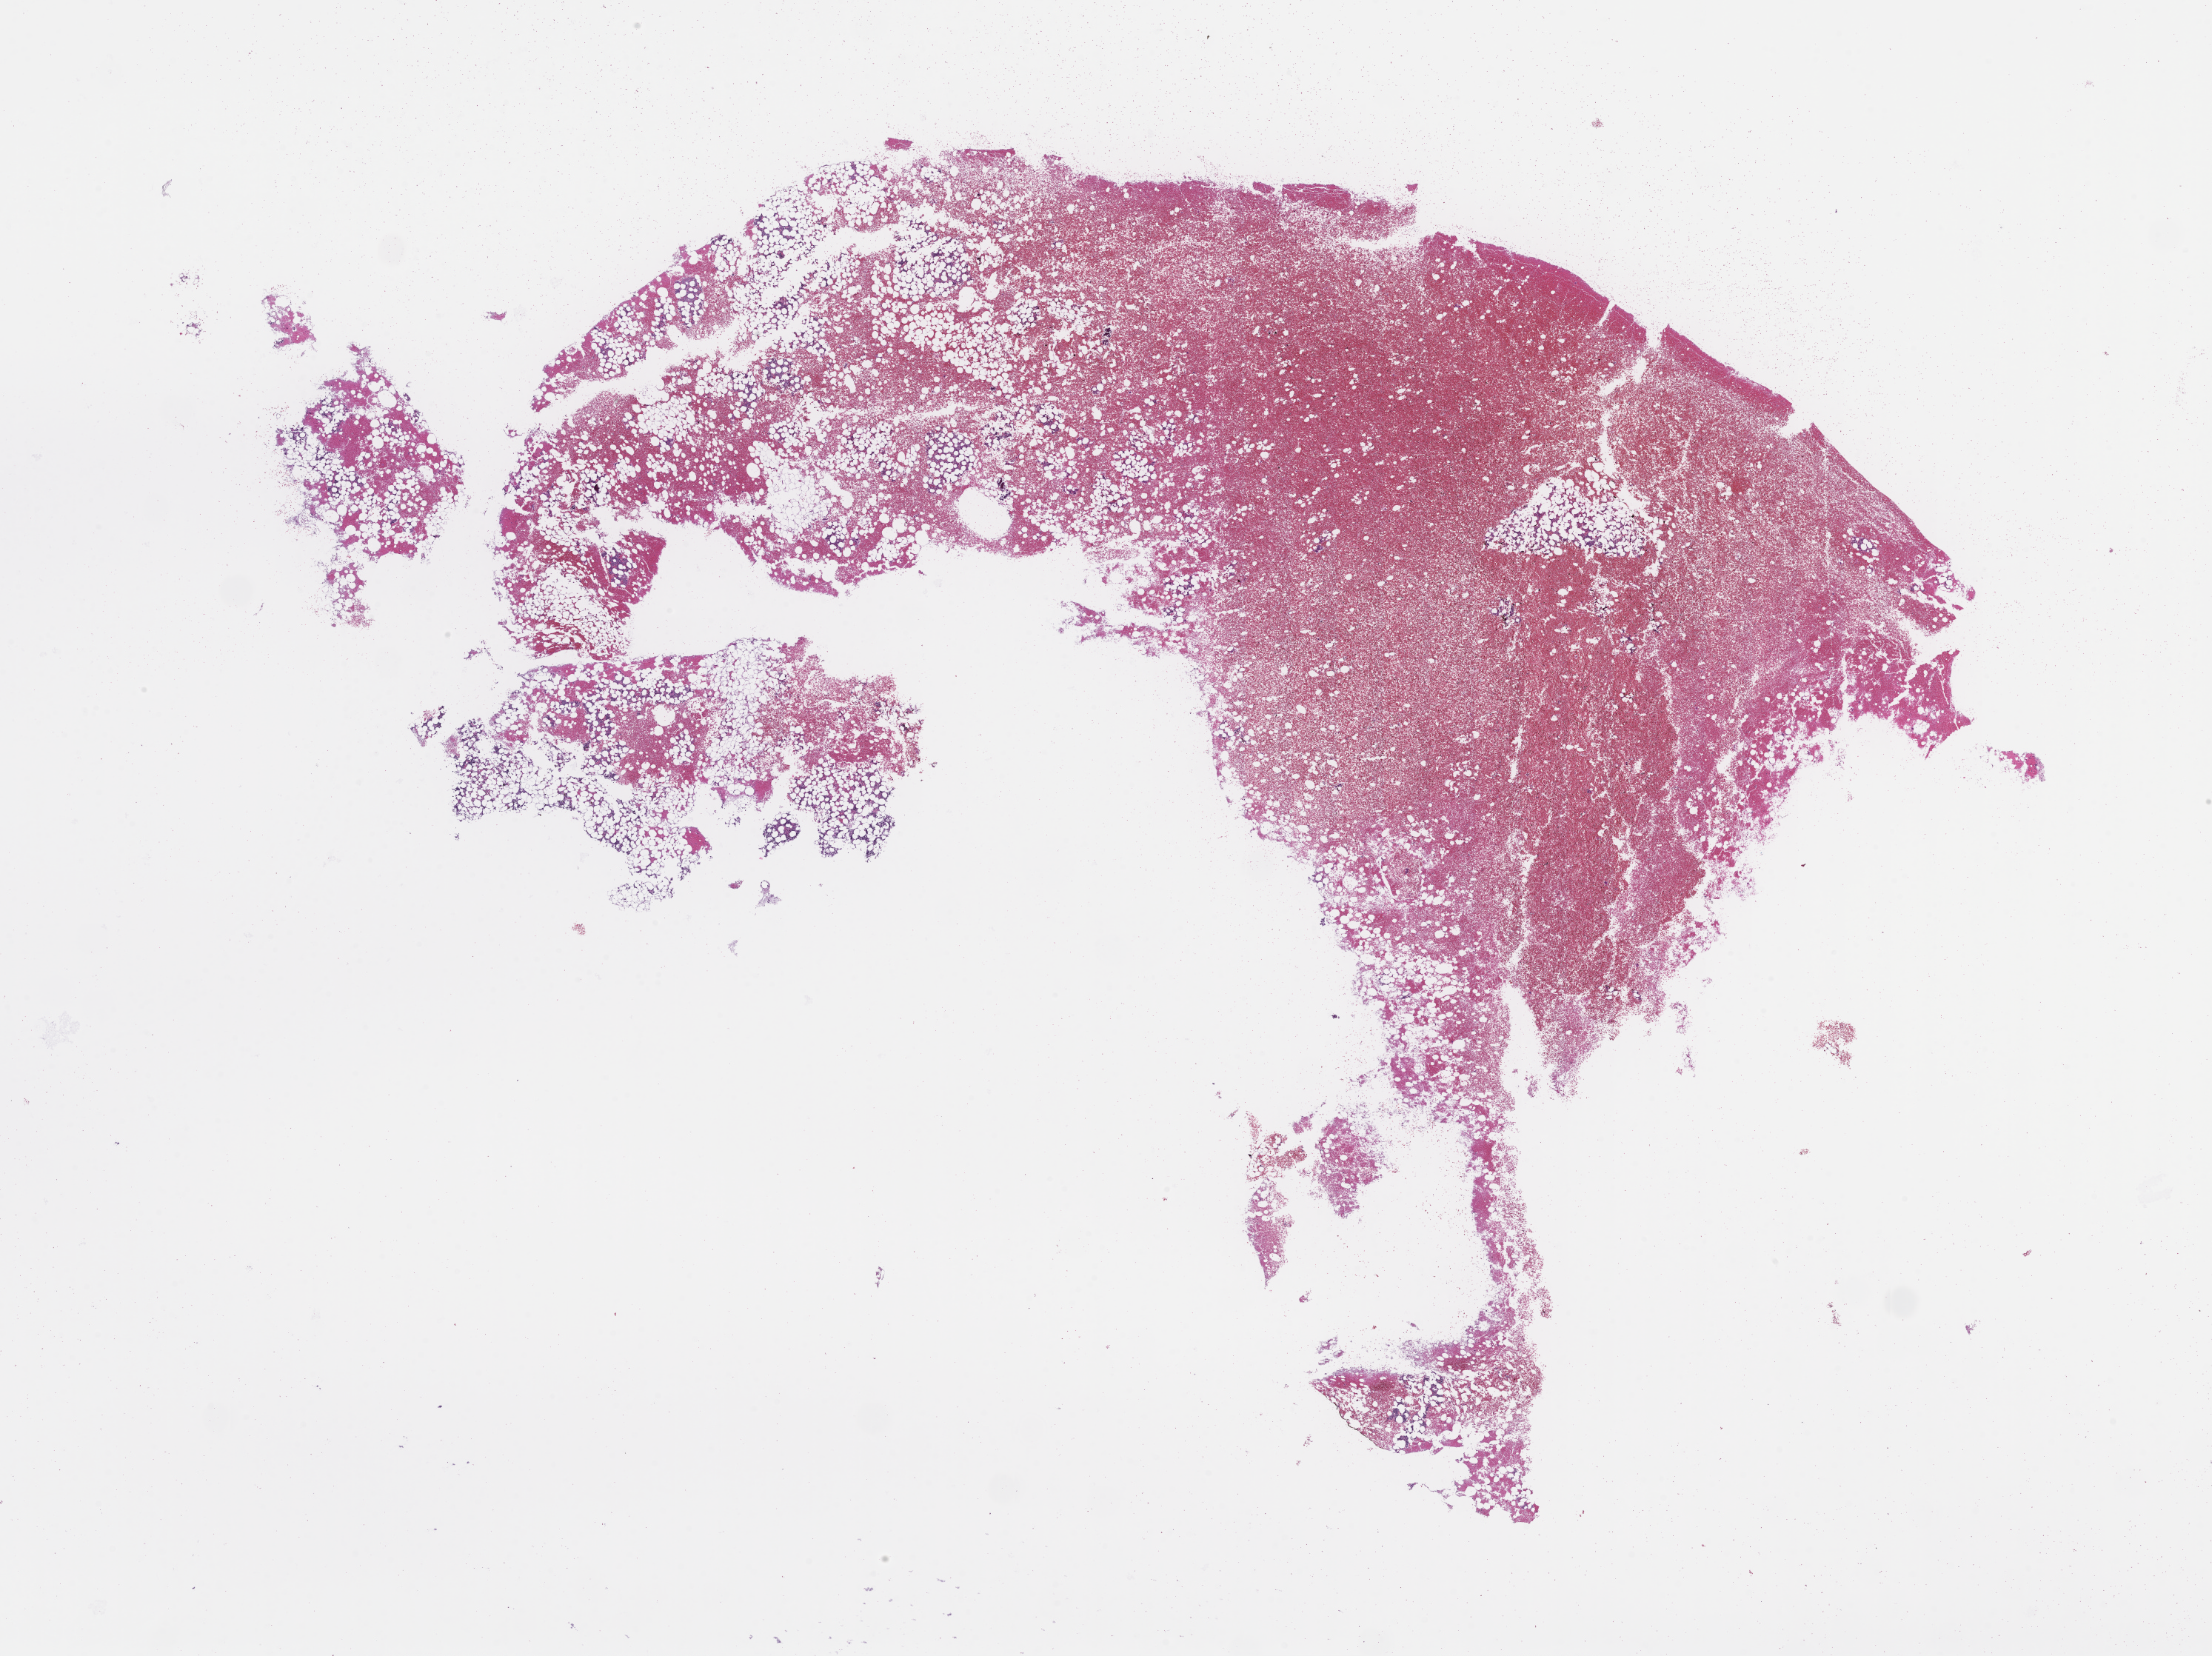
Whole-slide image, hematoxylin and eosin (H&E) stain, a low-resolution overview of the entire scanned area, about 24.1 x 18.1 mm; formalin-fixed paraffin-embedded section; tissue site: bone marrow. Male patient.
* from a patient with: Plasma Cell Myeloma